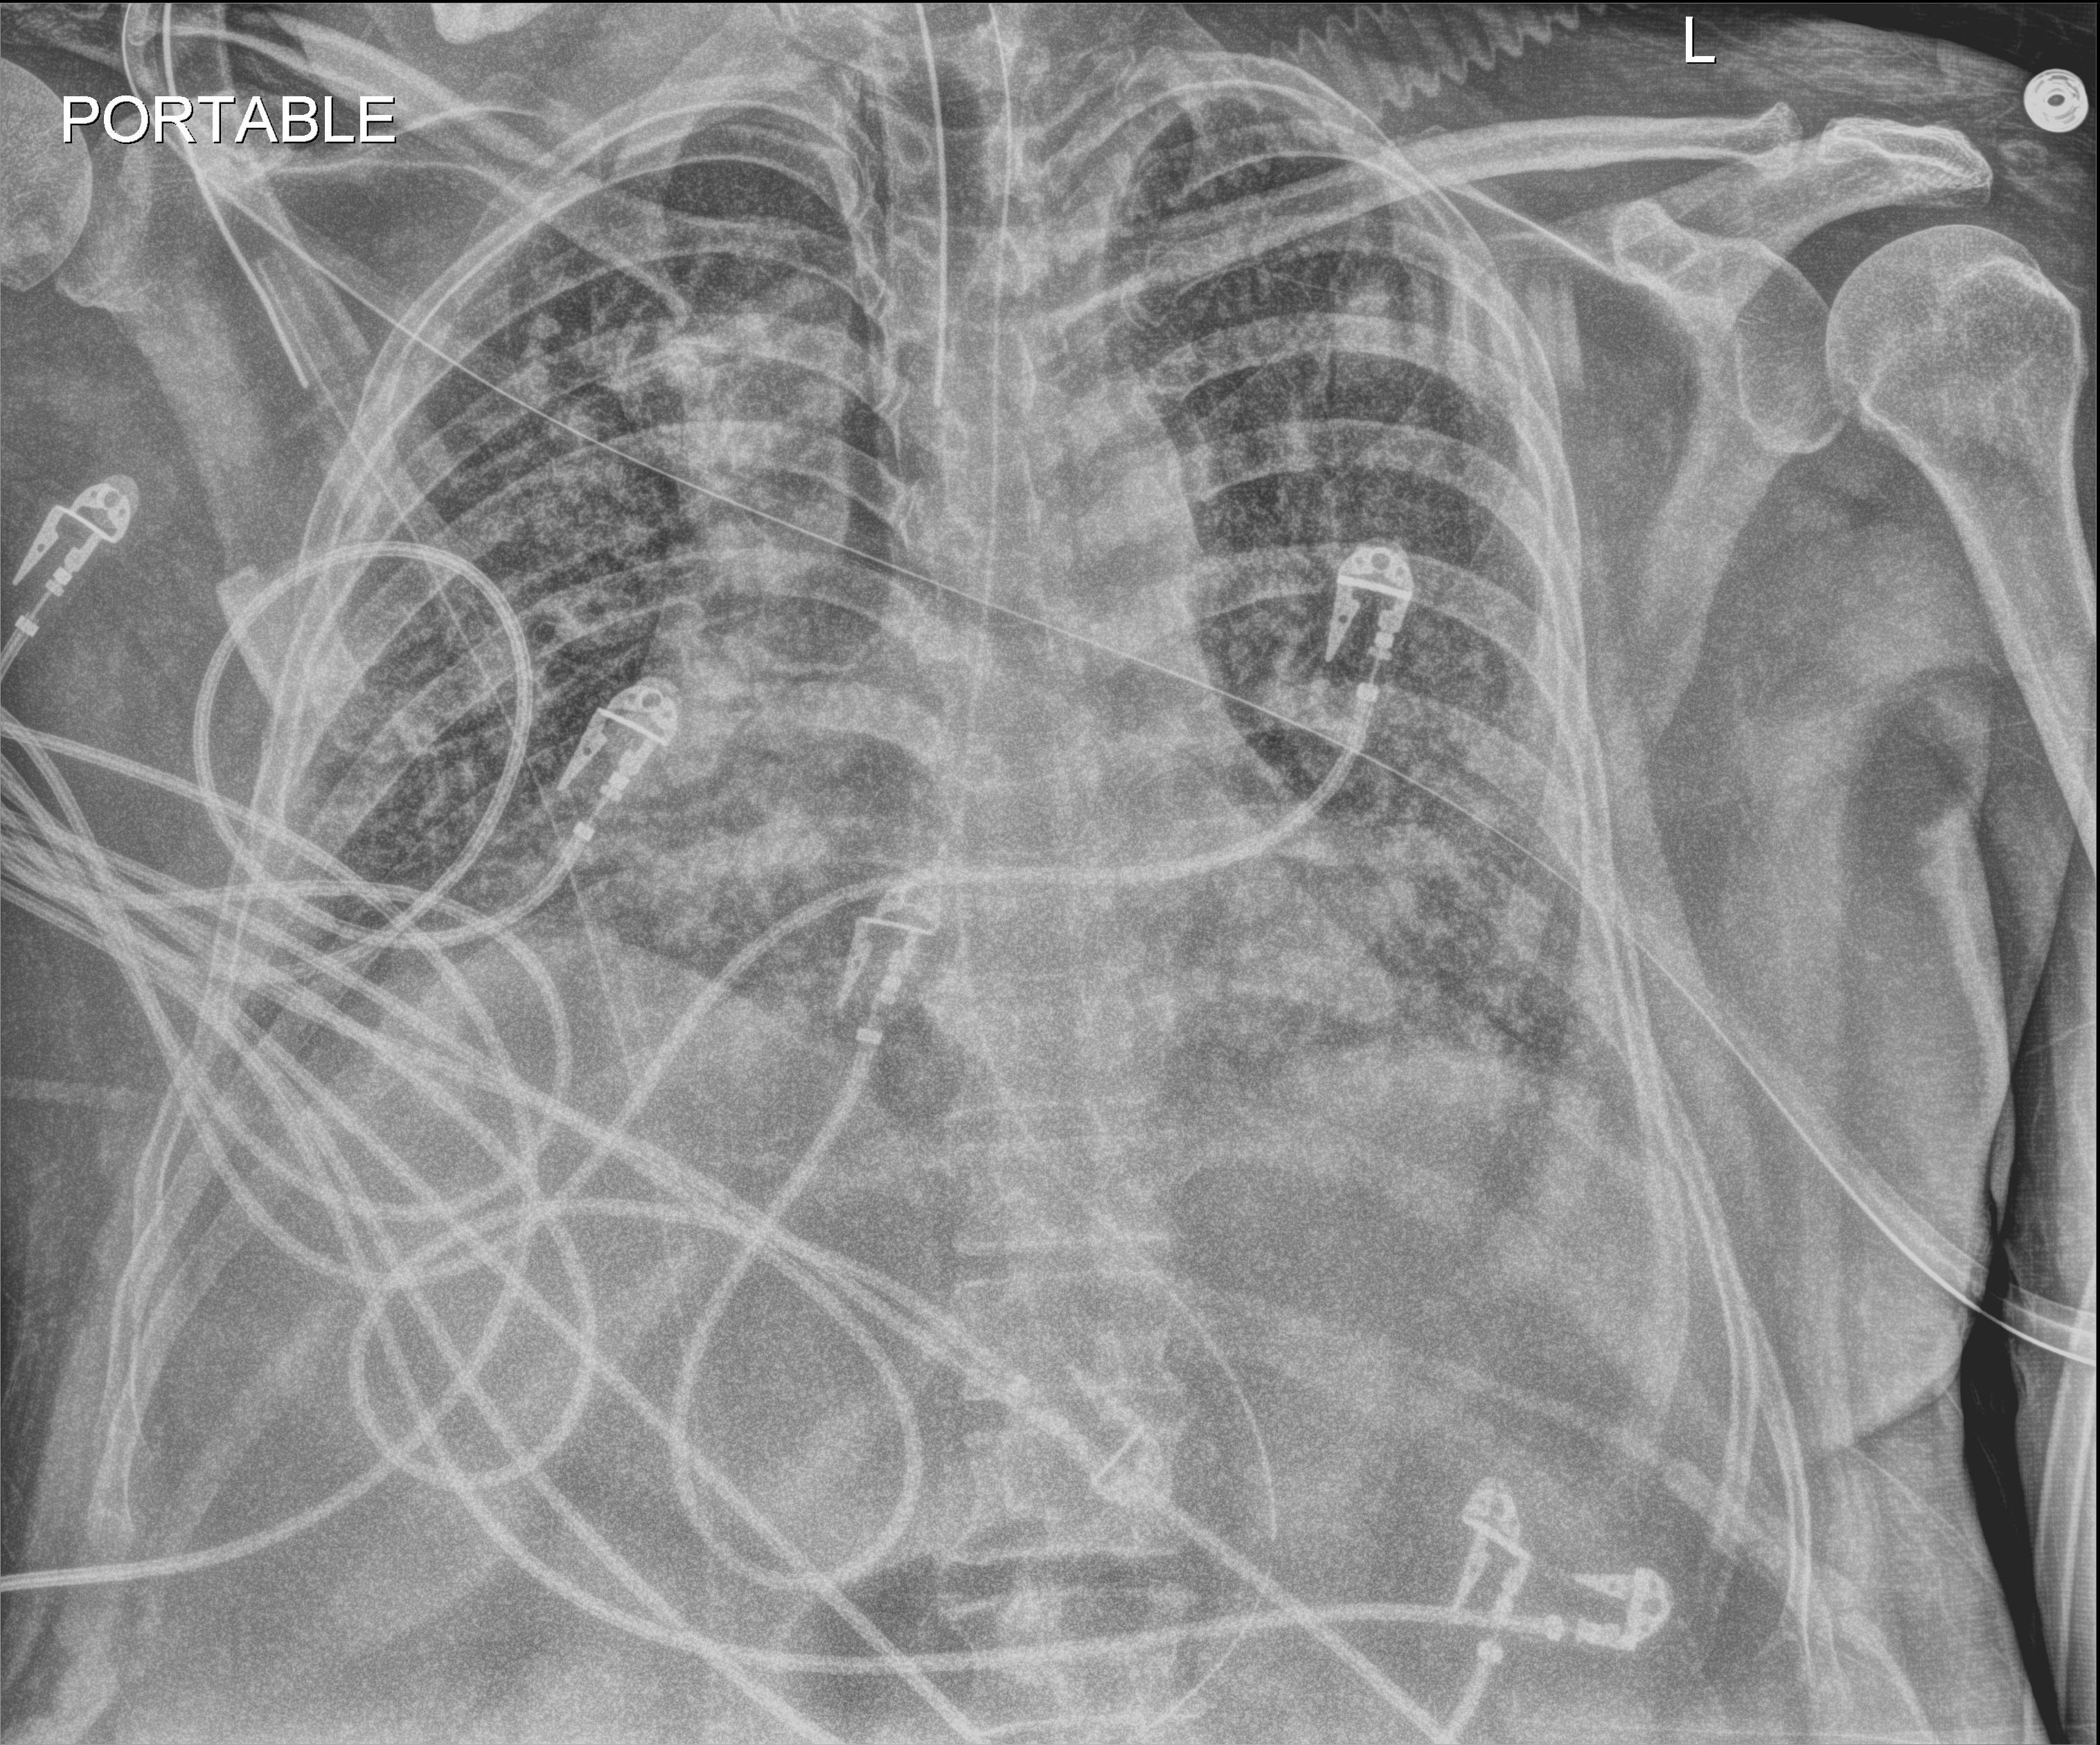
Portable chest radiograph; anteroposterior (AP) projection. Patient hospitalised with COVID-19, aged 18–59 years.
Admission-level facts for this patient (not findings on this image; timing relative to this image not recorded): mechanically ventilated during this hospital stay: yes.